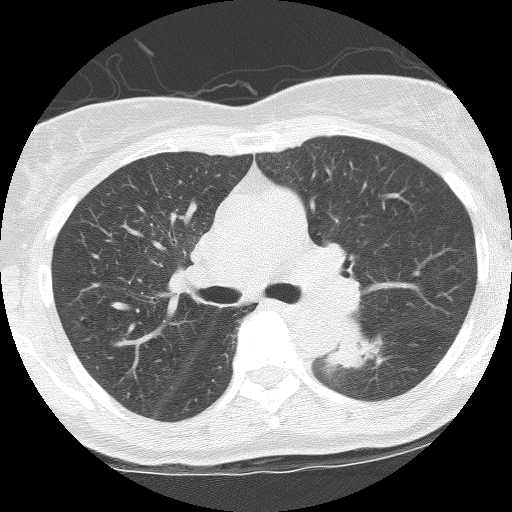
Axial slice from a low-dose chest CT screening exam; third annual screen; lung window (W 1500 / L -600 HU); 2.5 mm slice thickness; 512 × 512 image matrix, field of view 290 × 290 mm. Female, age 62 years at enrolment. Former smoker at enrolment.
• Lesion marked by an expert reader, bounding box <322,328,388,369> (left, top, right, bottom; pixels).
• The screening reader recorded 3 non-calcified nodules or masses ≥4 mm on this exam (right upper lobe, left lower lobe, left upper lobe); which of them this box marks is not recorded.
• Official screen result: positive, other.
• Participant outcome: lung cancer diagnosed 165 days after this screen — squamous cell carcinoma, NOS, left lower lobe, stage IIIB (AJCC 6th edition), 31 mm at pathology.